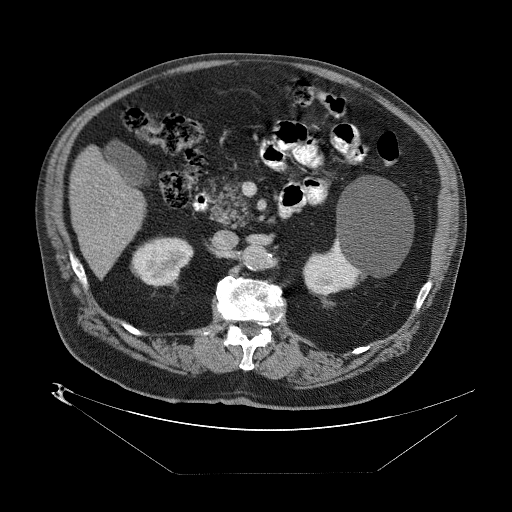
Contrast-enhanced abdominal CT (liver protocol), one axial slice; slice 25 of 89 in the series (ordered by position); reconstruction kernel STANDARD; 140 kVp; one of 2 acquisitions stored at this slice position; soft-tissue window (W 400 / L 40 HU); 2.5 mm slice thickness; 512 × 512 image matrix, field of view 480 × 480 mm. From the clinical record (not read from this slice): diagnosis: hepatocellular carcinoma (patient treated with transarterial chemoembolisation; whether this scan precedes or follows treatment is not stated here); TNM stage (as recorded): Stage-II; Child-Pugh class: B; tumour size: 4 cm.
Outlined on this slice (semi-automatically segmented with operator editing):
- abdominal aorta: bounding box <245,246,268,270> (left, top, right, bottom; pixels)
- liver parenchyma outside the tumour (the mass and vessels are separate outlines, so this box may not span the whole liver): <66,138,146,274>
- liver vessels: <86,207,119,254>